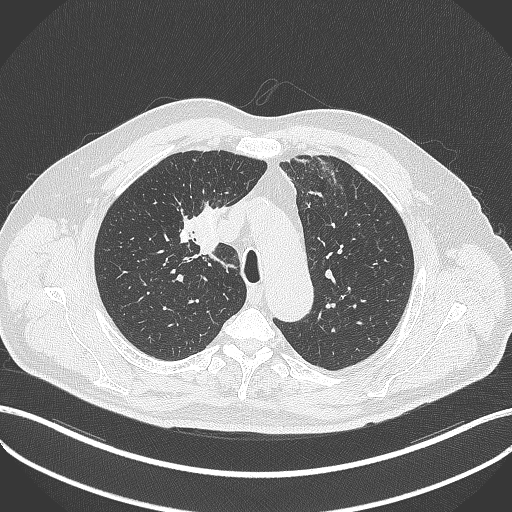
Chest CT, one axial slice; position 290 of 411 along the scan axis; reconstruction kernel B70f; lung window (W 1500 / L -600 HU); 512 × 512 image matrix, field of view 400 × 400 mm. Male patient, age 60 years. Case-level facts recorded for this patient, not image findings: clinical TNM (as recorded): T1b N1 M0.
Annotated regions visible in this slice (bounding box drawn by a radiologist):
- lung tumour (recorded histology: squamous cell carcinoma): bounding box (x1, y1, x2, y2) in pixels: (192, 197, 223, 261)